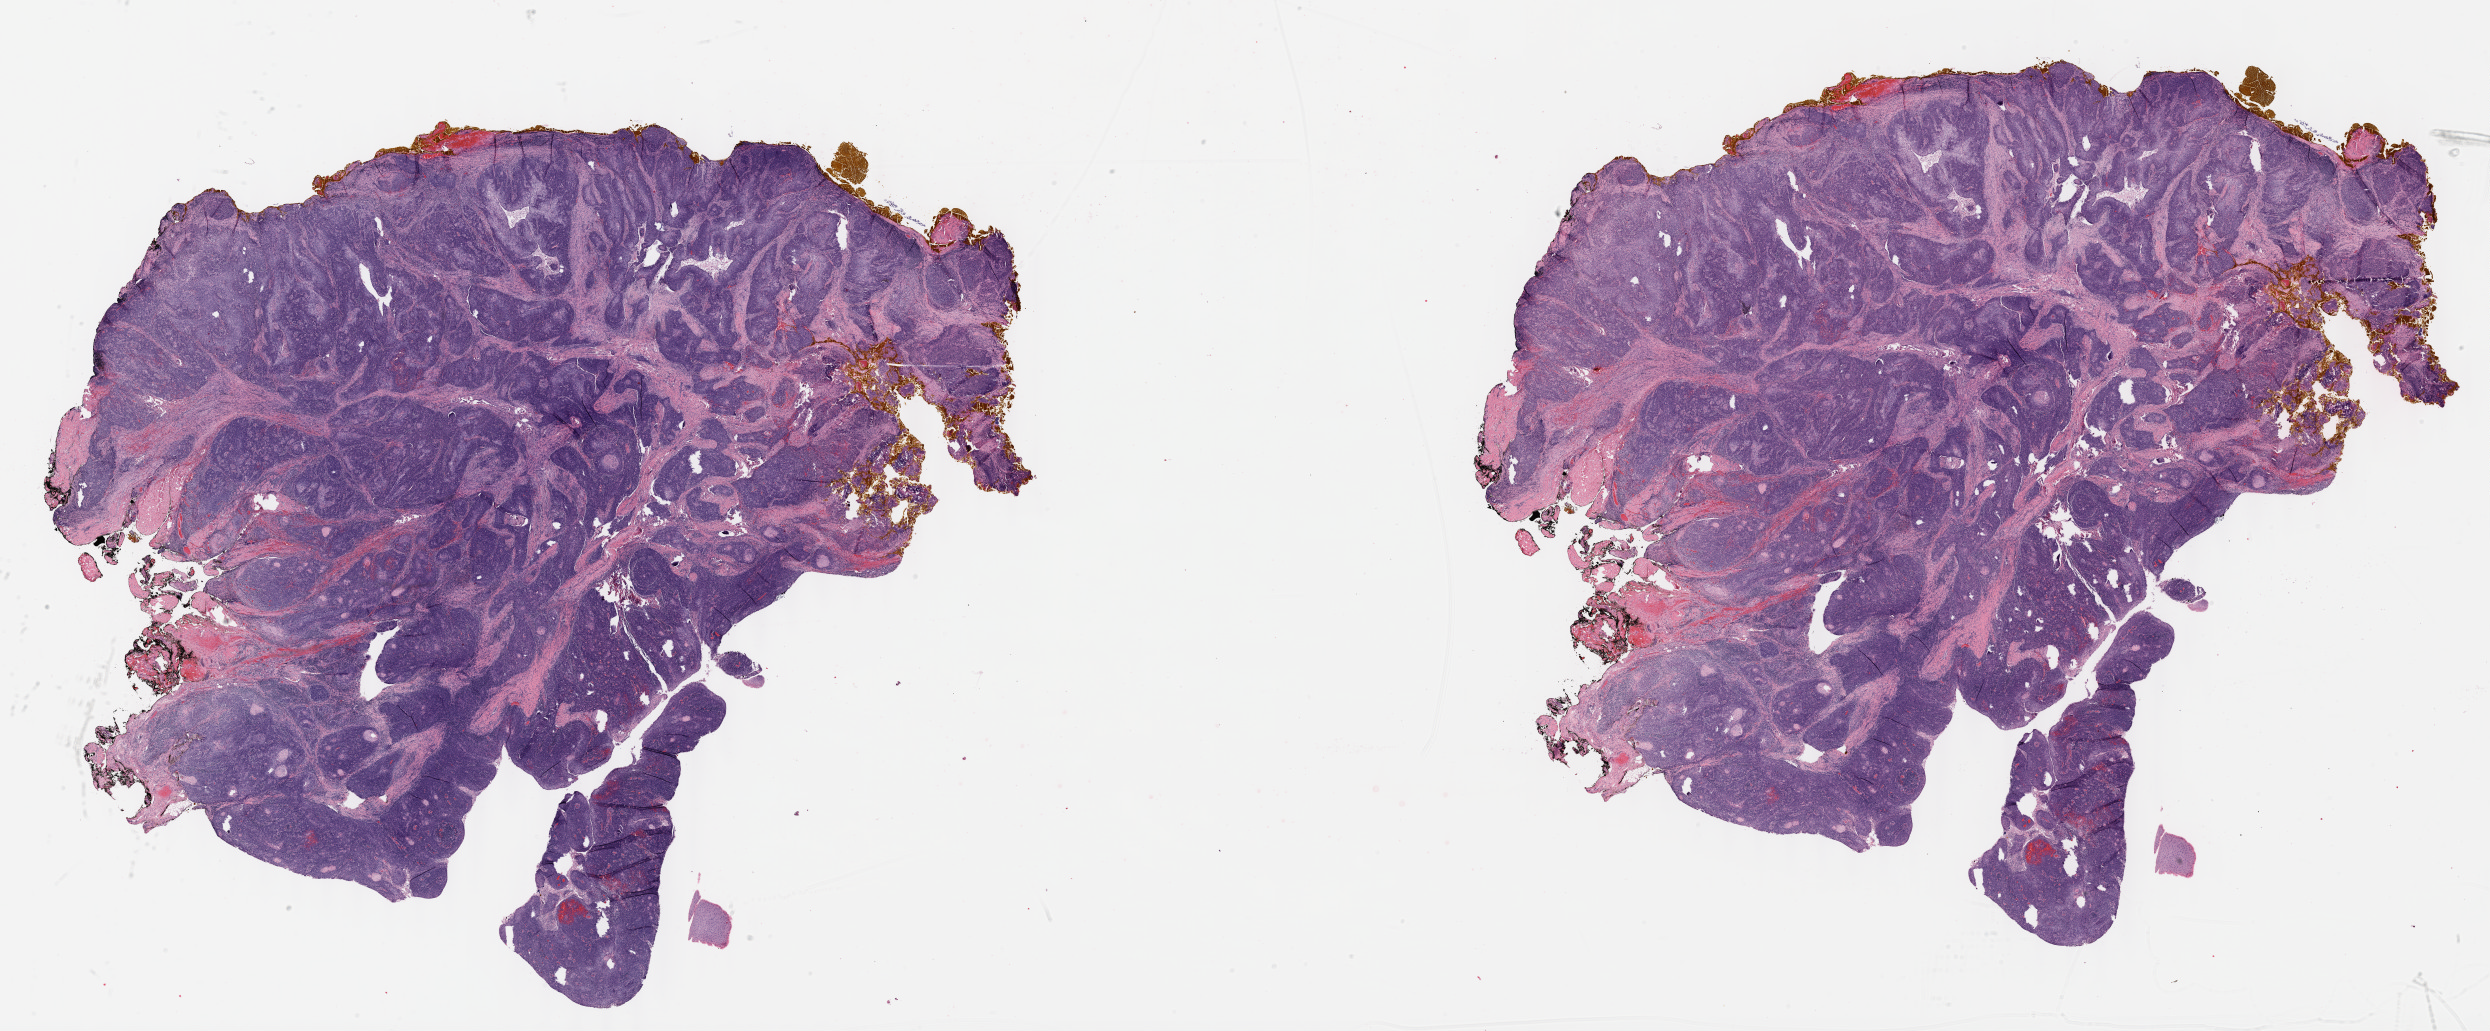
Whole-slide histology image, H&E-stained, a low-resolution overview of the entire scanned area, about 40.2 x 16.7 mm (acquisition: 40x scan), FFPE section, primary tumour sample from the head and neck. Patient: female, age at initial diagnosis 55 years. Histologic grade: G2 (moderately differentiated).
Histologic diagnosis: Squamous cell carcinoma, NOS (tonsil, NOS). Laterality: left. AJCC pathologic stage: IVA.